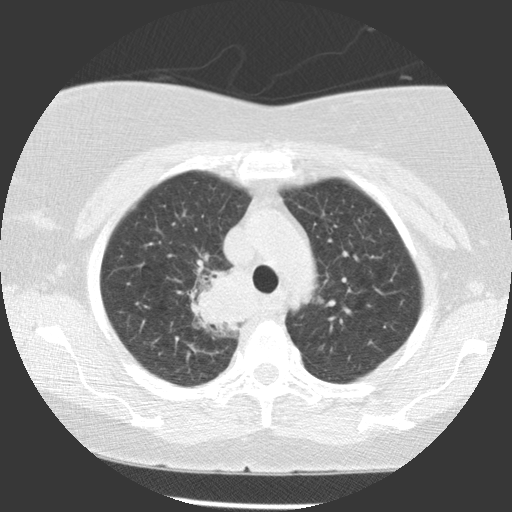
Low-dose screening chest CT, one axial slice; slice 89 of 116 in the series (ordered by position); lung window (W 1500 / L -600 HU); 2.5 mm slice thickness; 512 × 512 image matrix, field of view 320 × 320 mm.
Outlined on this slice (outlined manually by an expert reader):
- lesion 1 (tumor, upper lobe of right lung): bounding box (x1, y1, x2, y2) in pixels: (190, 267, 254, 334)